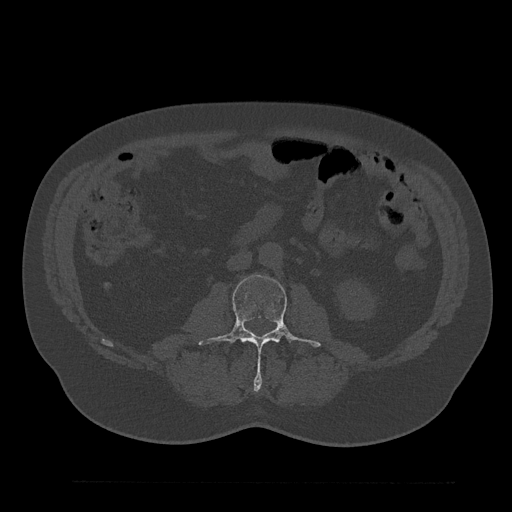
CT including the spine, one axial slice; slice 35 of 797 in the series (ordered by position); 120 kVp; bone window (W 1800 / L 400 HU); 512 × 512 image matrix. Patient: male, 61 years. From the clinical record (not read from this slice): primary cancer: prostate.
Structures marked on this image (semi-automatic segmentation, software-assisted and operator-edited):
- L3 vertebra: box from (x=198, y=274) to (x=321, y=390) px